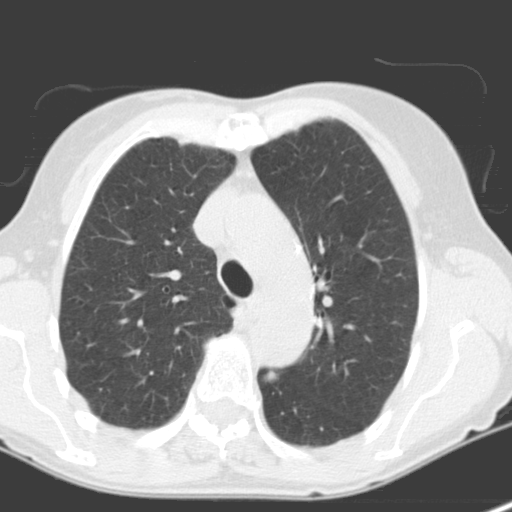
Low-dose screening chest CT, one axial slice. Position 105 of 141 along the scan axis. 120 kVp. Lung window (W 1500 / L -600 HU). 3.2 mm slice thickness. 512 × 512 image matrix, field of view 262 × 262 mm.
Structures marked on this image (expert manual segmentation):
- lesion 1 (tumor, lower lobe of left lung): bounding box <266,369,279,382> (left, top, right, bottom; pixels)